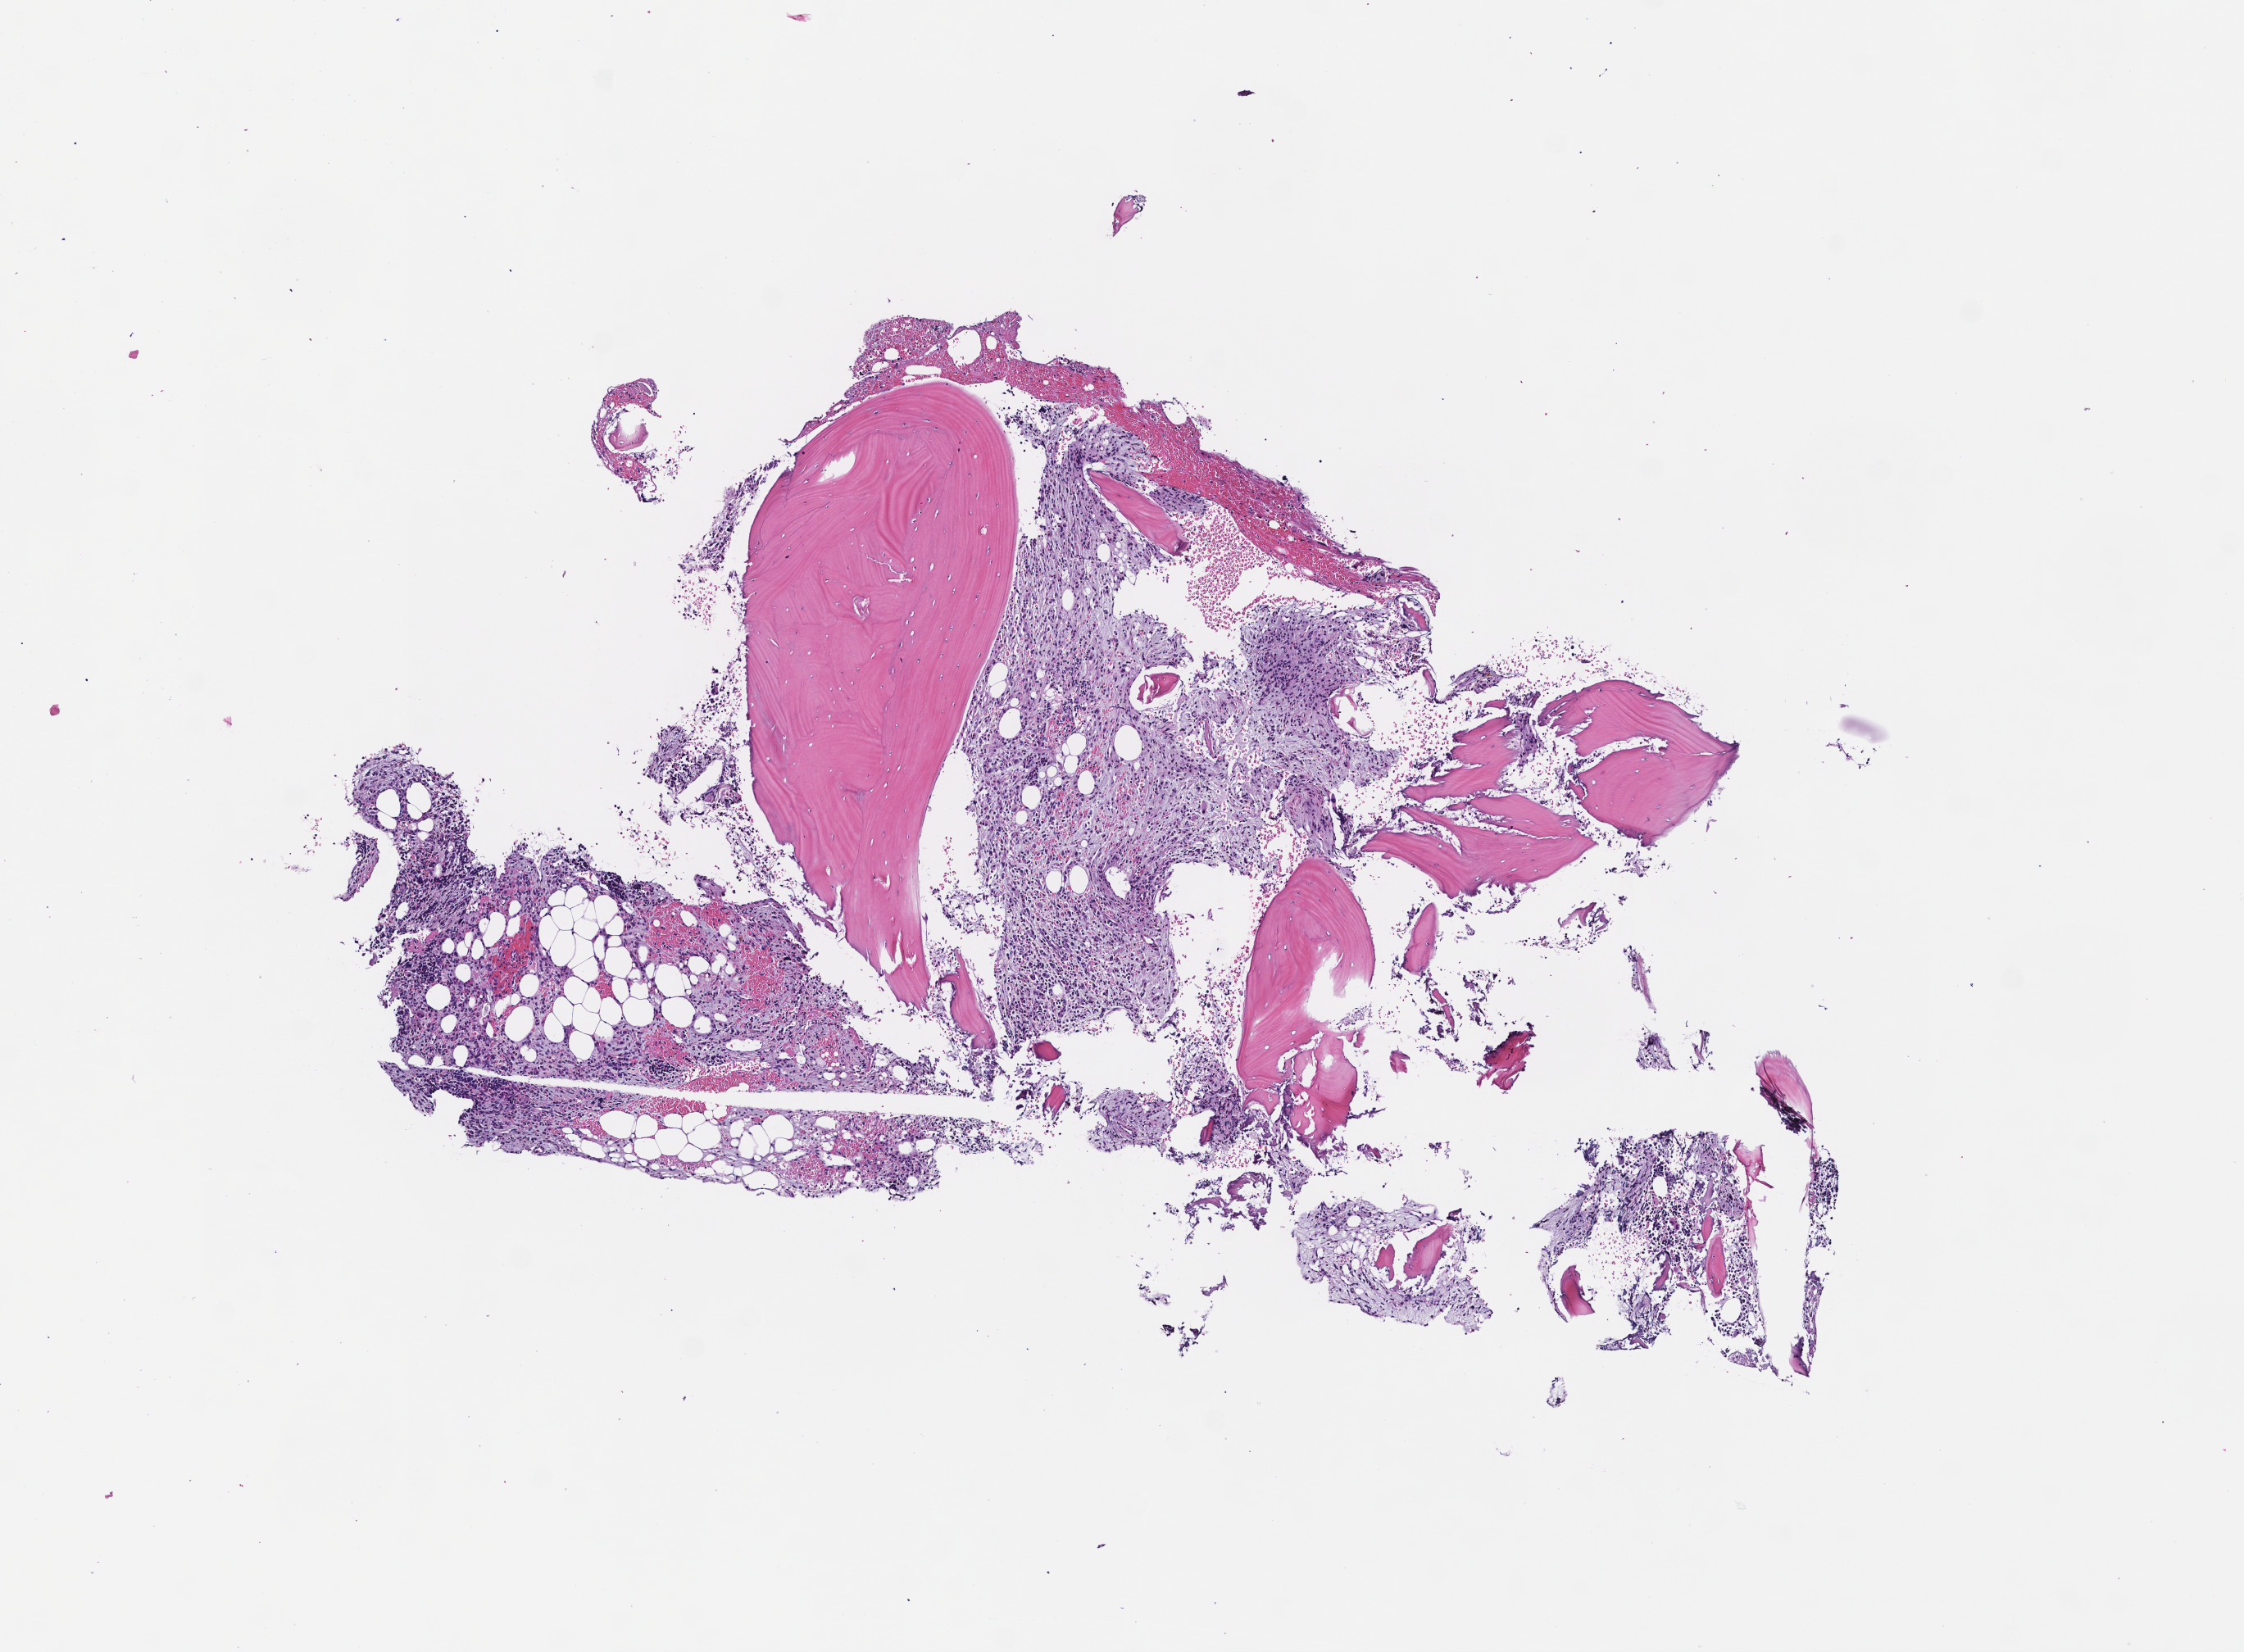
Whole-slide image, haematoxylin and eosin stain — low-resolution overview of the scanned area, about 5.5 x 4.1 mm, formalin-fixed paraffin-embedded section, site: bone marrow. Patient sex: female.
This section: primary tumor. Diagnosis: Plasma Cell Myeloma.